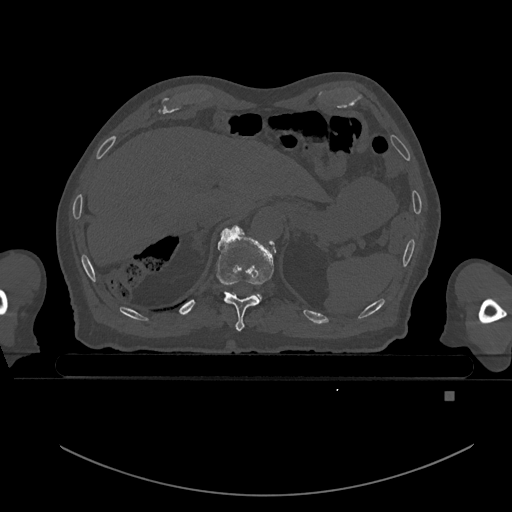
CT including the spine, one axial slice; position 77 of 969 along the scan axis; bone window (W 1800 / L 400 HU); 0.5 mm slice thickness; 512 × 512 image matrix, field of view 456 × 456 mm. Male patient, age 82 years. From the clinical record (not read from this slice): primary cancer: prostate.
Outlined on this slice (semi-automatically segmented with operator editing):
- T10 vertebra: bounding box <216,226,275,331> (left, top, right, bottom; pixels)
- T11 vertebra: <254,294,261,301>